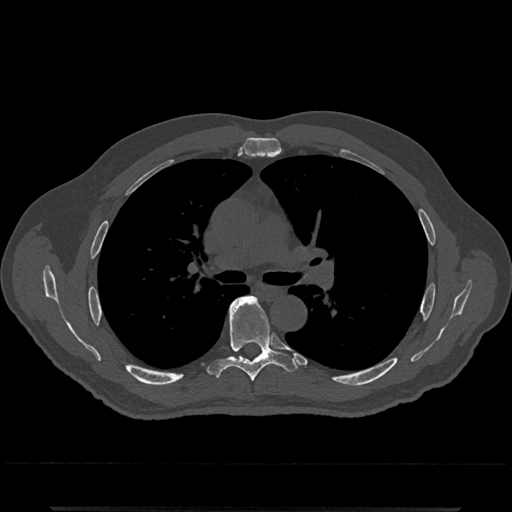
CT including the spine, one axial slice. Position 777 of 797 along the scan axis. Reconstruction kernel Br40s/3. 120 kVp. Bone window (W 1800 / L 400 HU). 0.5 mm slice thickness. 512 × 512 image matrix, field of view 393 × 393 mm. Patient: male, 67 years. Case-level facts recorded for this patient, not image findings: primary cancer: prostate.
Annotated regions visible in this slice (semi-automatically segmented with operator editing):
- T6 vertebra: bounding box (x1, y1, x2, y2) in pixels: (207, 296, 297, 382)